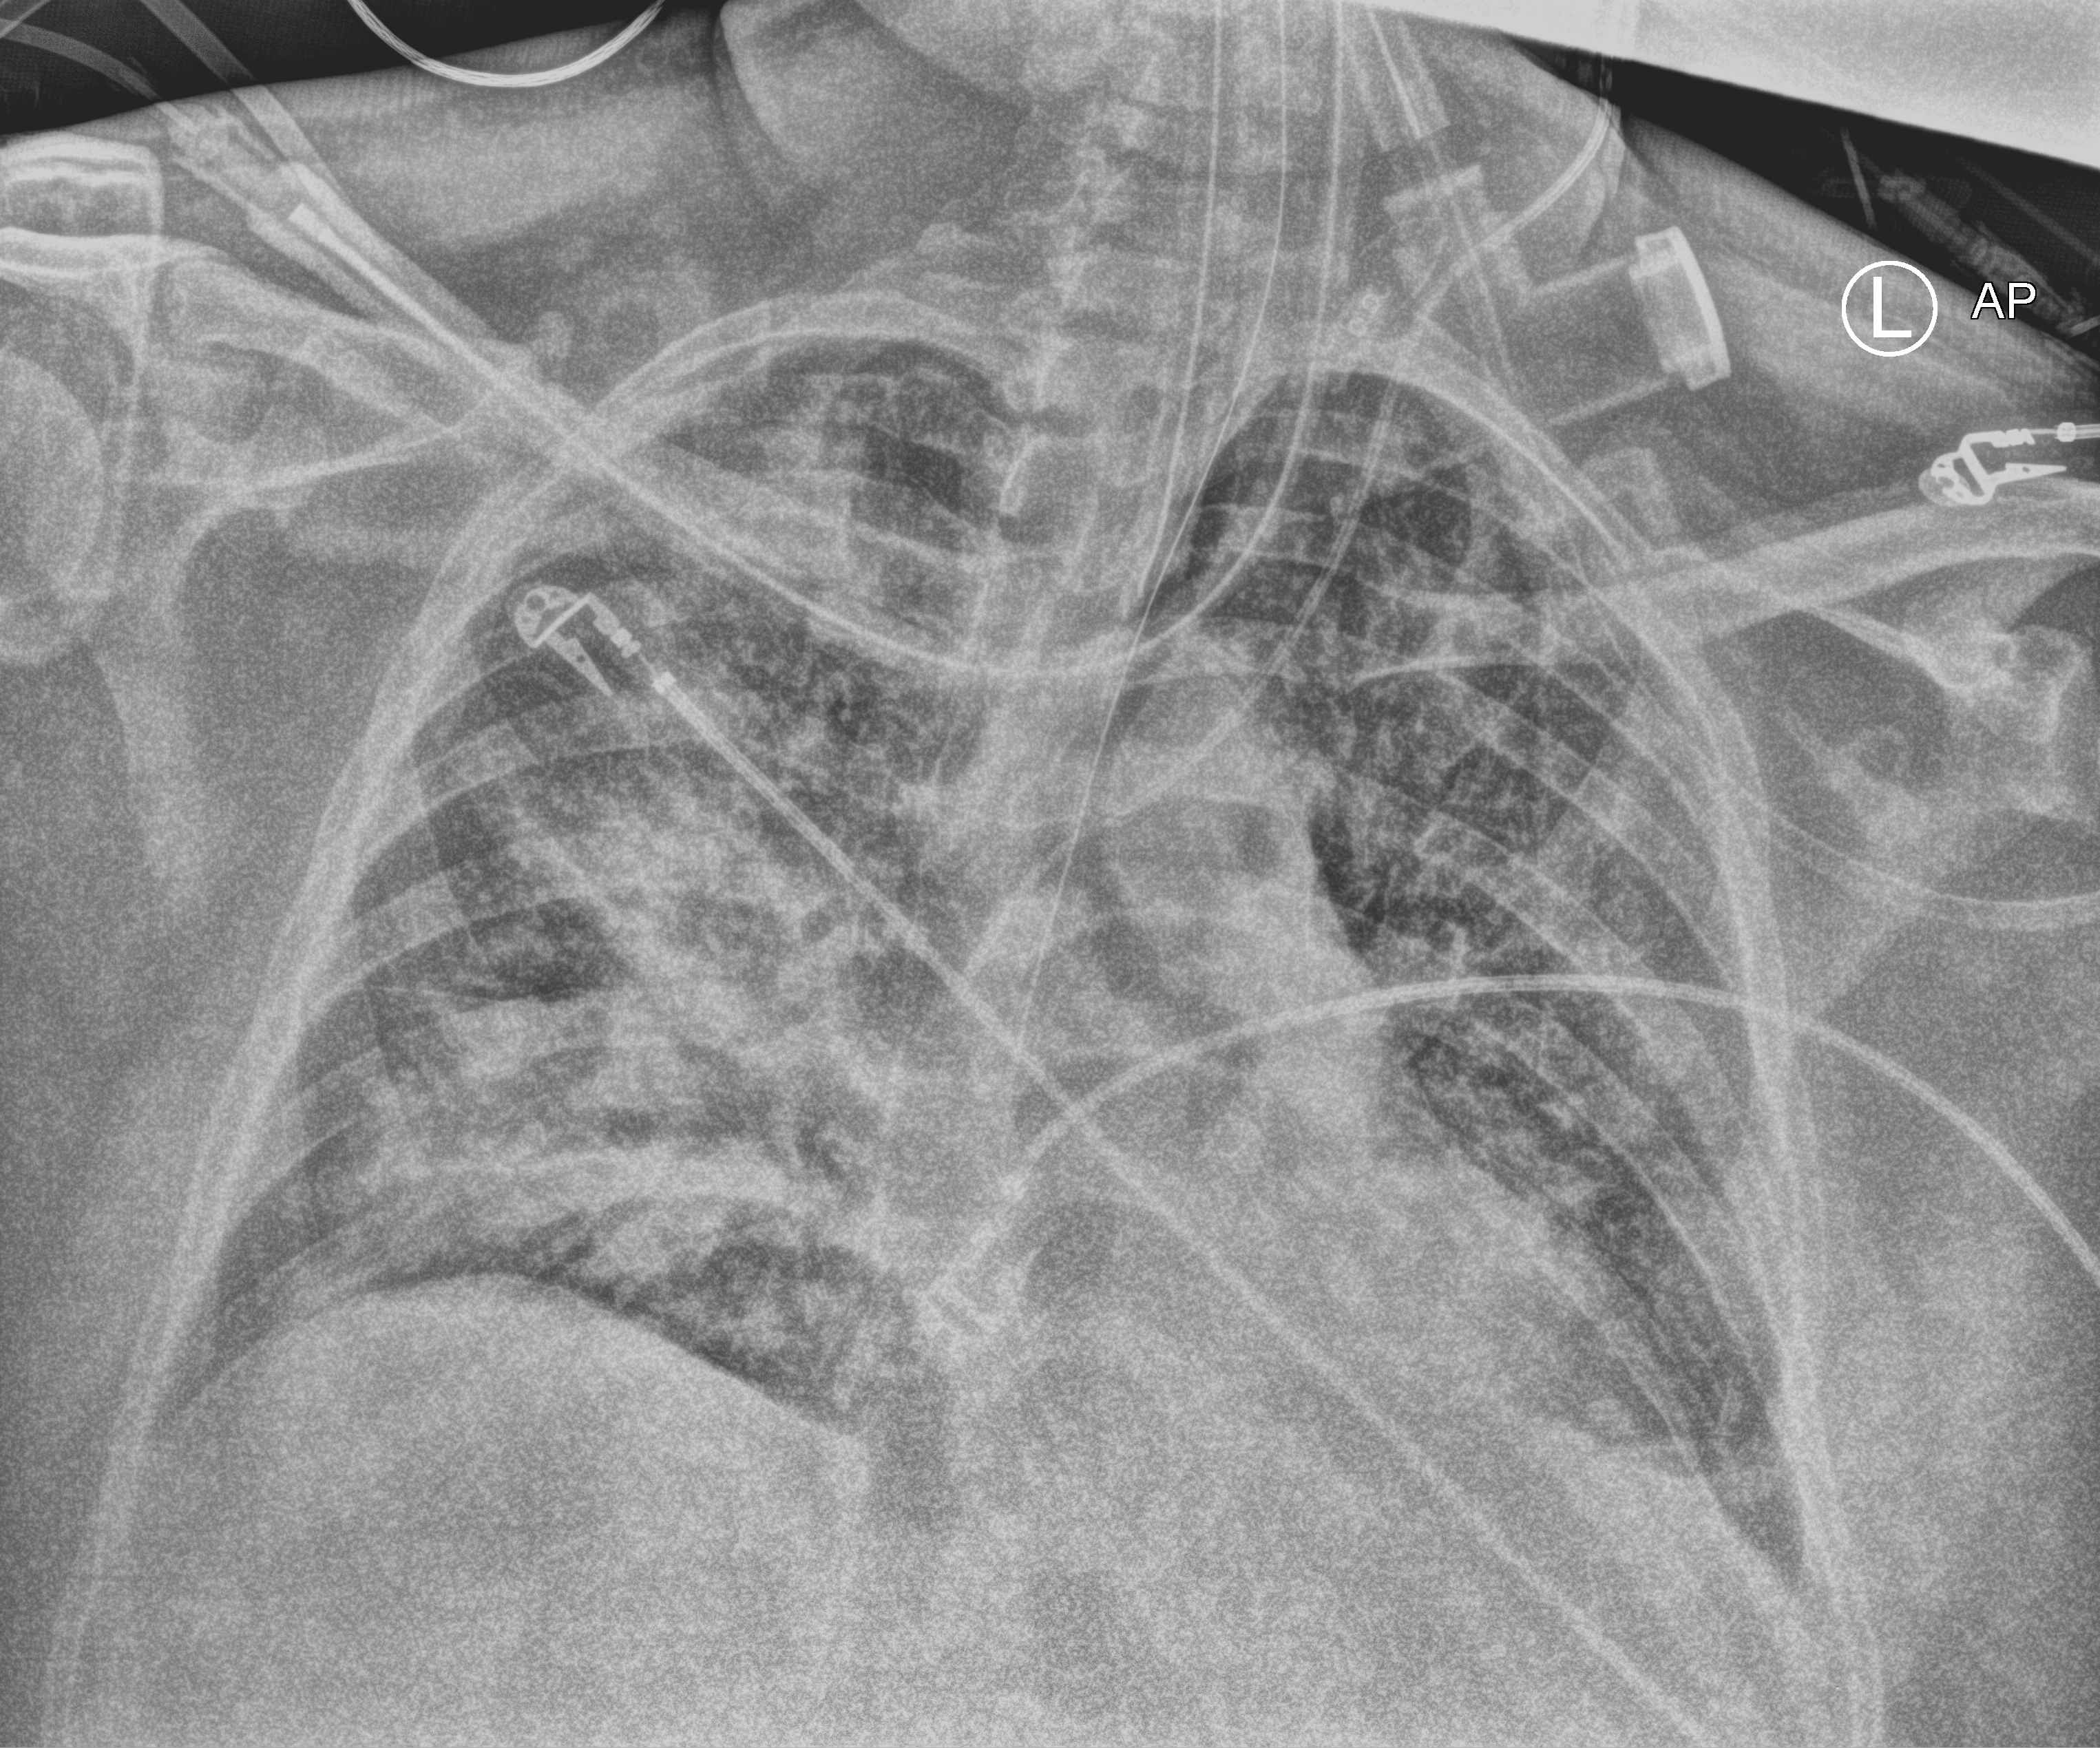
Bedside chest radiograph (computed radiography); anteroposterior (AP) projection. Patient hospitalised with COVID-19, aged 18–59 years.
From the hospital-stay record, not from the radiograph (when in the stay this image was taken is not recorded): admitted to intensive care during this hospital stay: yes.